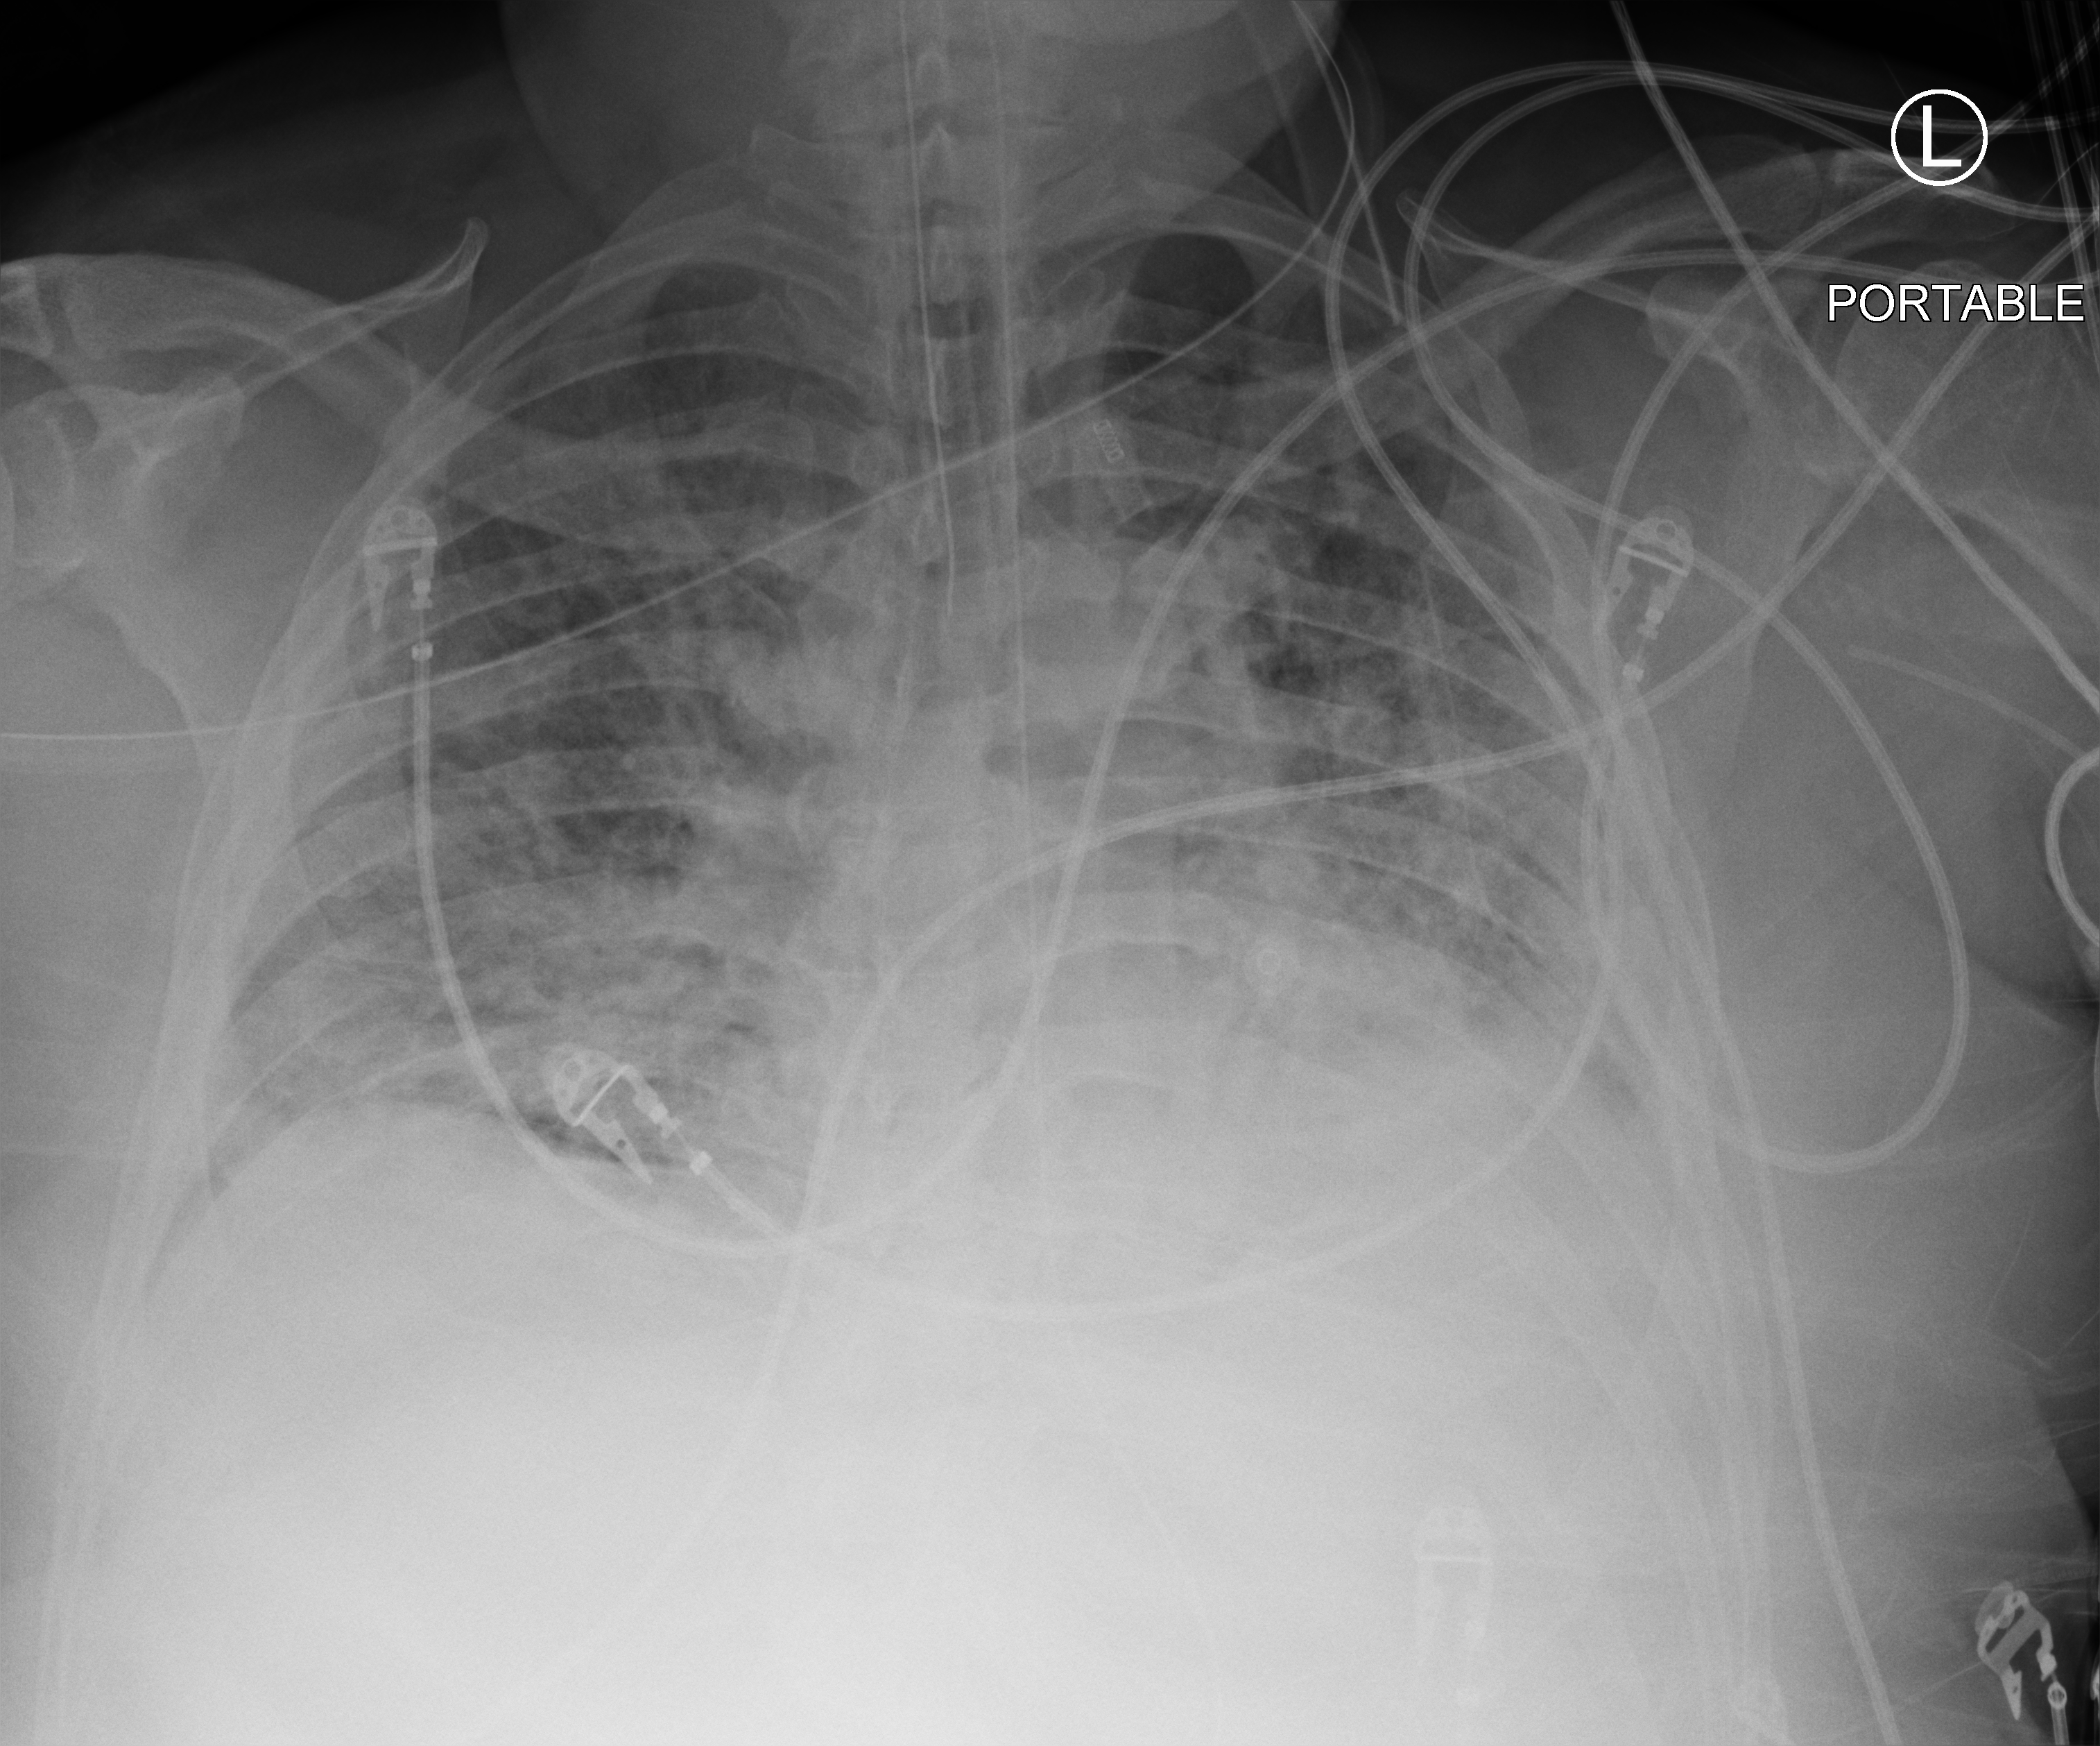
Chest X-ray (portable). Male patient hospitalised with COVID-19, age 18–59 years.
Hospital-stay facts (about this admission, not read from this image; timing relative to this image not recorded): COPD (admission record): no; mechanically ventilated during this hospital stay: yes; hypertension (admission record): yes.